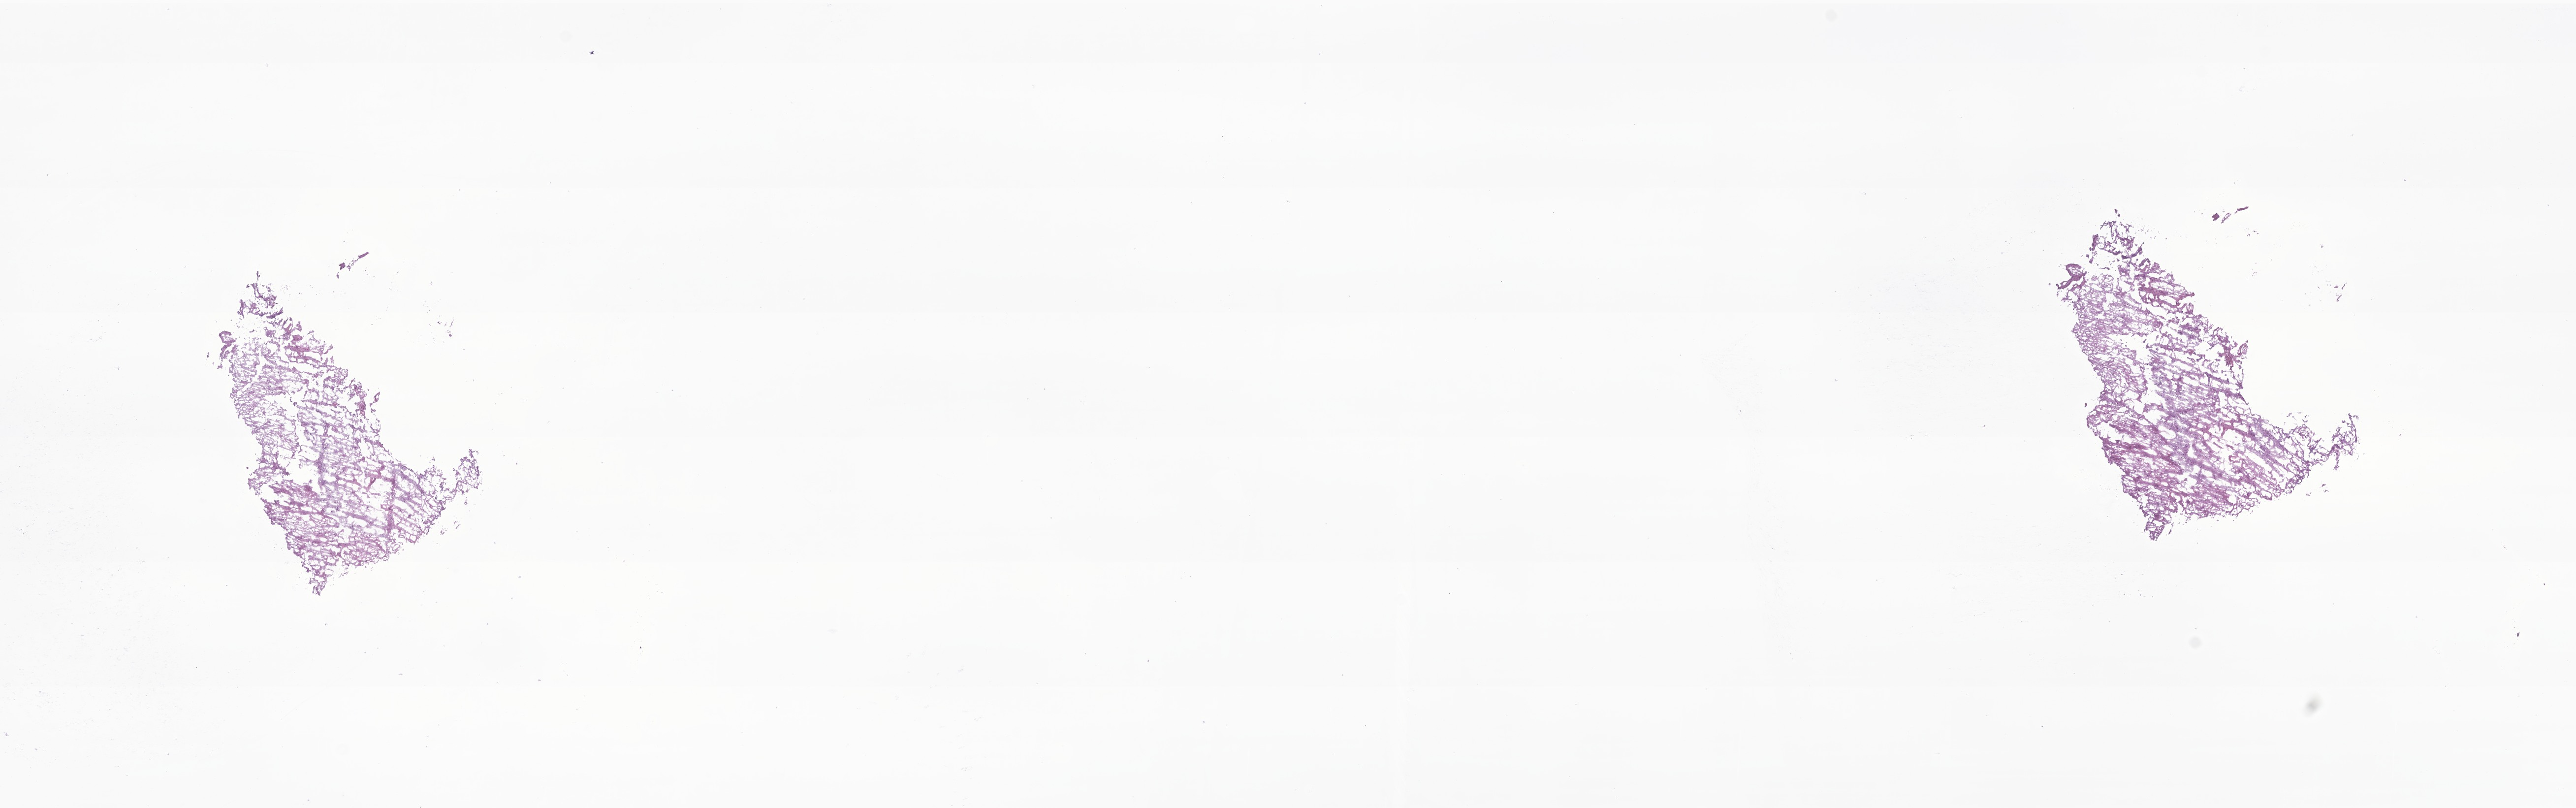
Whole-slide image, H&E stain of tumor tissue from the brain — a low-resolution overview of the entire scanned area, about 22.1 x 6.9 mm; frozen section. Female patient, age 66 months (5 years 6 months).
Diagnosis (ICD-O-3 morphology term): Astrocytoma, NOS.